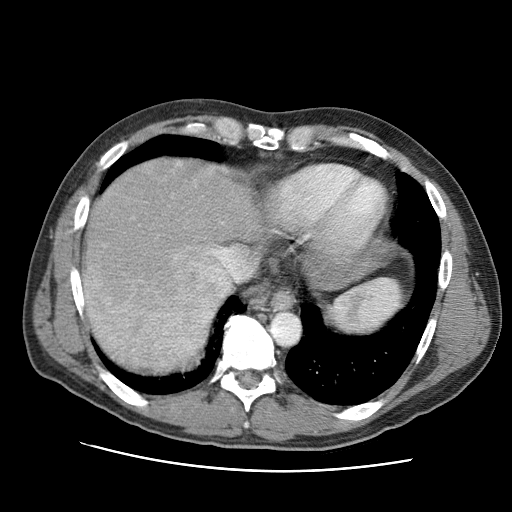
Contrast-enhanced abdominal CT (liver protocol), one axial slice; slice 81 of 95 in the series (ordered by position); reconstruction kernel STANDARD; 120 kVp; one of 2 acquisitions stored at this slice position; soft-tissue window (W 400 / L 40 HU); 512 × 512 image matrix. Case-level facts recorded for this patient, not image findings: diagnosis: hepatocellular carcinoma (patient treated with transarterial chemoembolisation; whether this scan precedes or follows treatment is not stated here); TNM stage (as recorded): Stage-IVA; Child-Pugh class: A; tumour differentiation: moderately differentiated; tumour nodularity: multinodular.
Annotated regions visible in this slice (semi-automatic segmentation, software-assisted and operator-edited):
- liver parenchyma outside the tumour (the mass and vessels are separate outlines, so this box may not span the whole liver): bounding box (x1, y1, x2, y2) in pixels: (82, 158, 262, 343)
- mass: (82, 253, 232, 375)
- liver vessels: (174, 163, 251, 277)